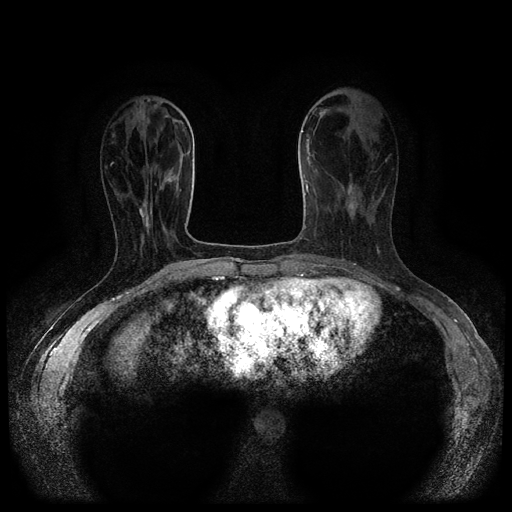
Breast MRI (dynamic contrast-enhanced, multi-phase), one axial slice. Position 34 of 116 along the scan axis. Dynamic contrast-enhanced series, time point 2 of 5 at this slice position (early post-contrast). 1.5 T. TE 2.6 ms, TR 5.4 ms. 2 mm slice thickness. 512 × 512 image matrix. Patient: female, 47 years.
Outlined on this slice (semi-automatically segmented with operator editing):
- breast lesion (labelled 'tumour' in the annotation; benign lesions carry a separate 'benign' label): bounding box <347,183,356,213> (left, top, right, bottom; pixels)
- breast lesion (labelled 'tumour' in the annotation; benign lesions carry a separate 'benign' label): <136,197,152,234>